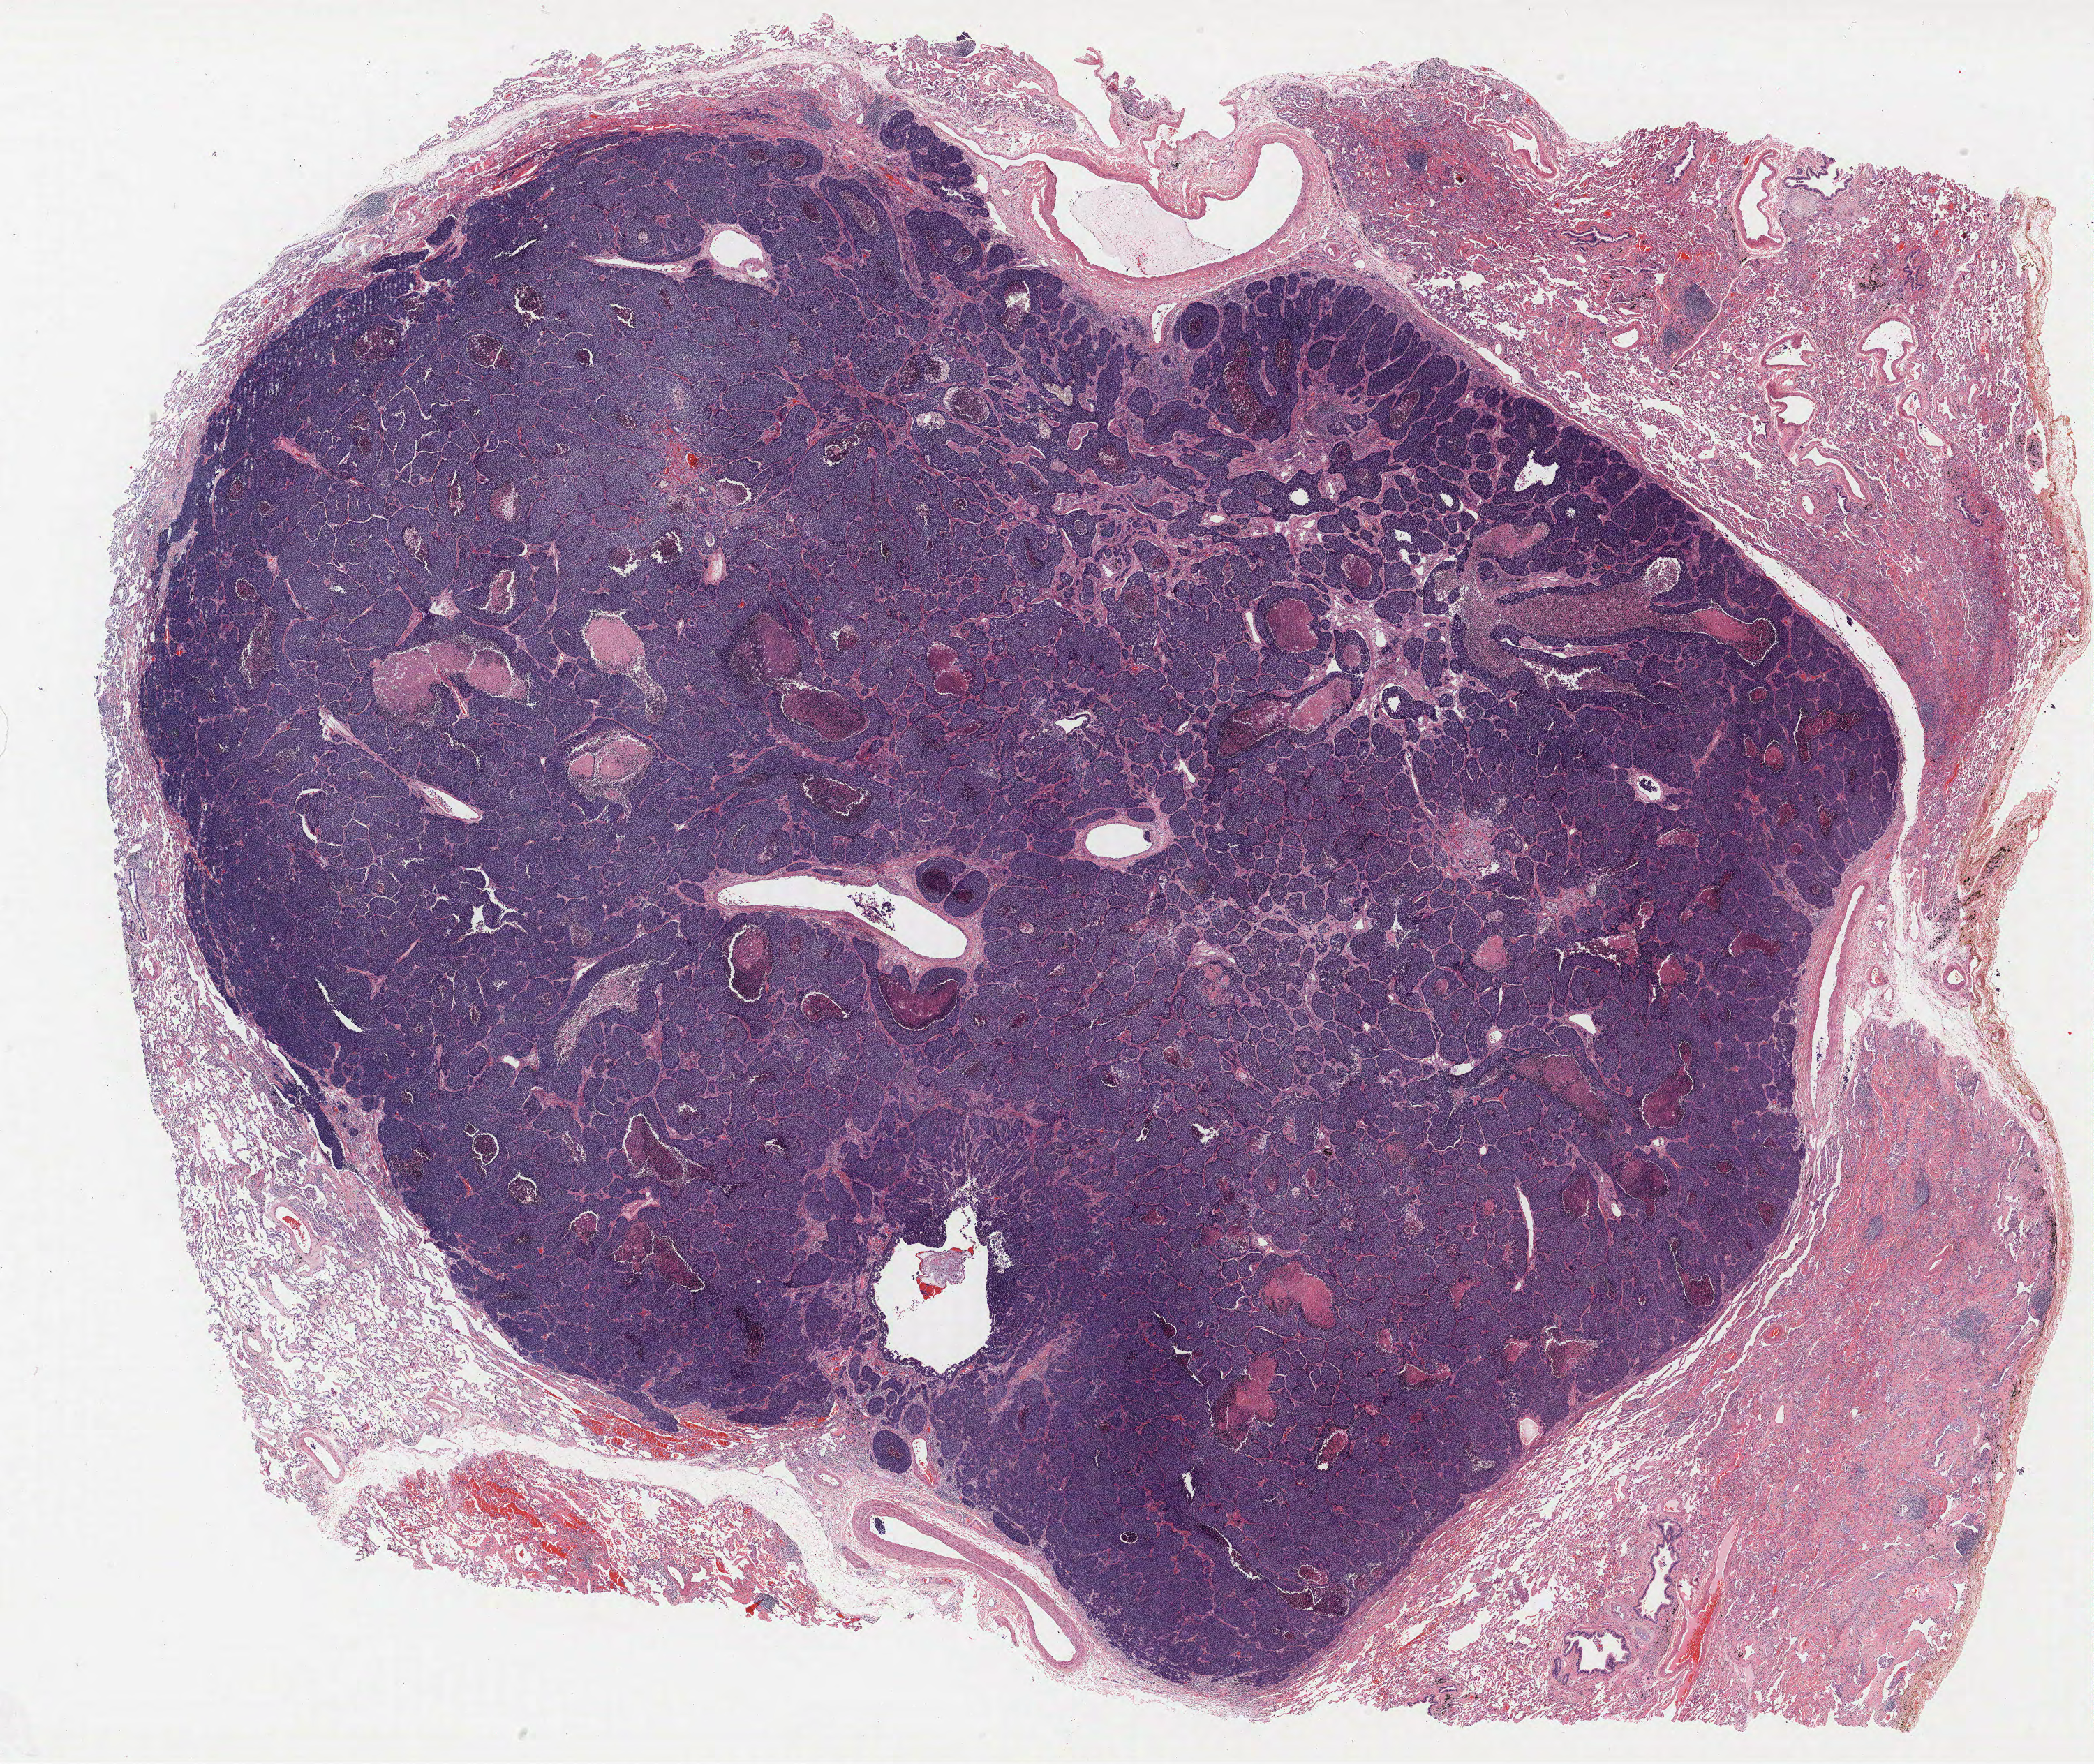
H&E whole-slide image, shown as a low-resolution overview of the whole scanned area (about 24.0 x 20.2 mm, slide scanned at 40x). Formalin-fixed paraffin-embedded (FFPE) section. Lung tissue. Male, age 68 at enrolment. Current smoker at enrolment. Grade: undifferentiated (G4).
Stage (AJCC 6th edition): IA. Participant's lung-cancer diagnosis: Large cell neuroendocrine carcinoma (ICD-O-3 8013/3). Primary tumour location (clinical record): lingula. Tumour size (pathology): 25 mm. ICD-O-3 topography: upper lobe of lung (C34.1).